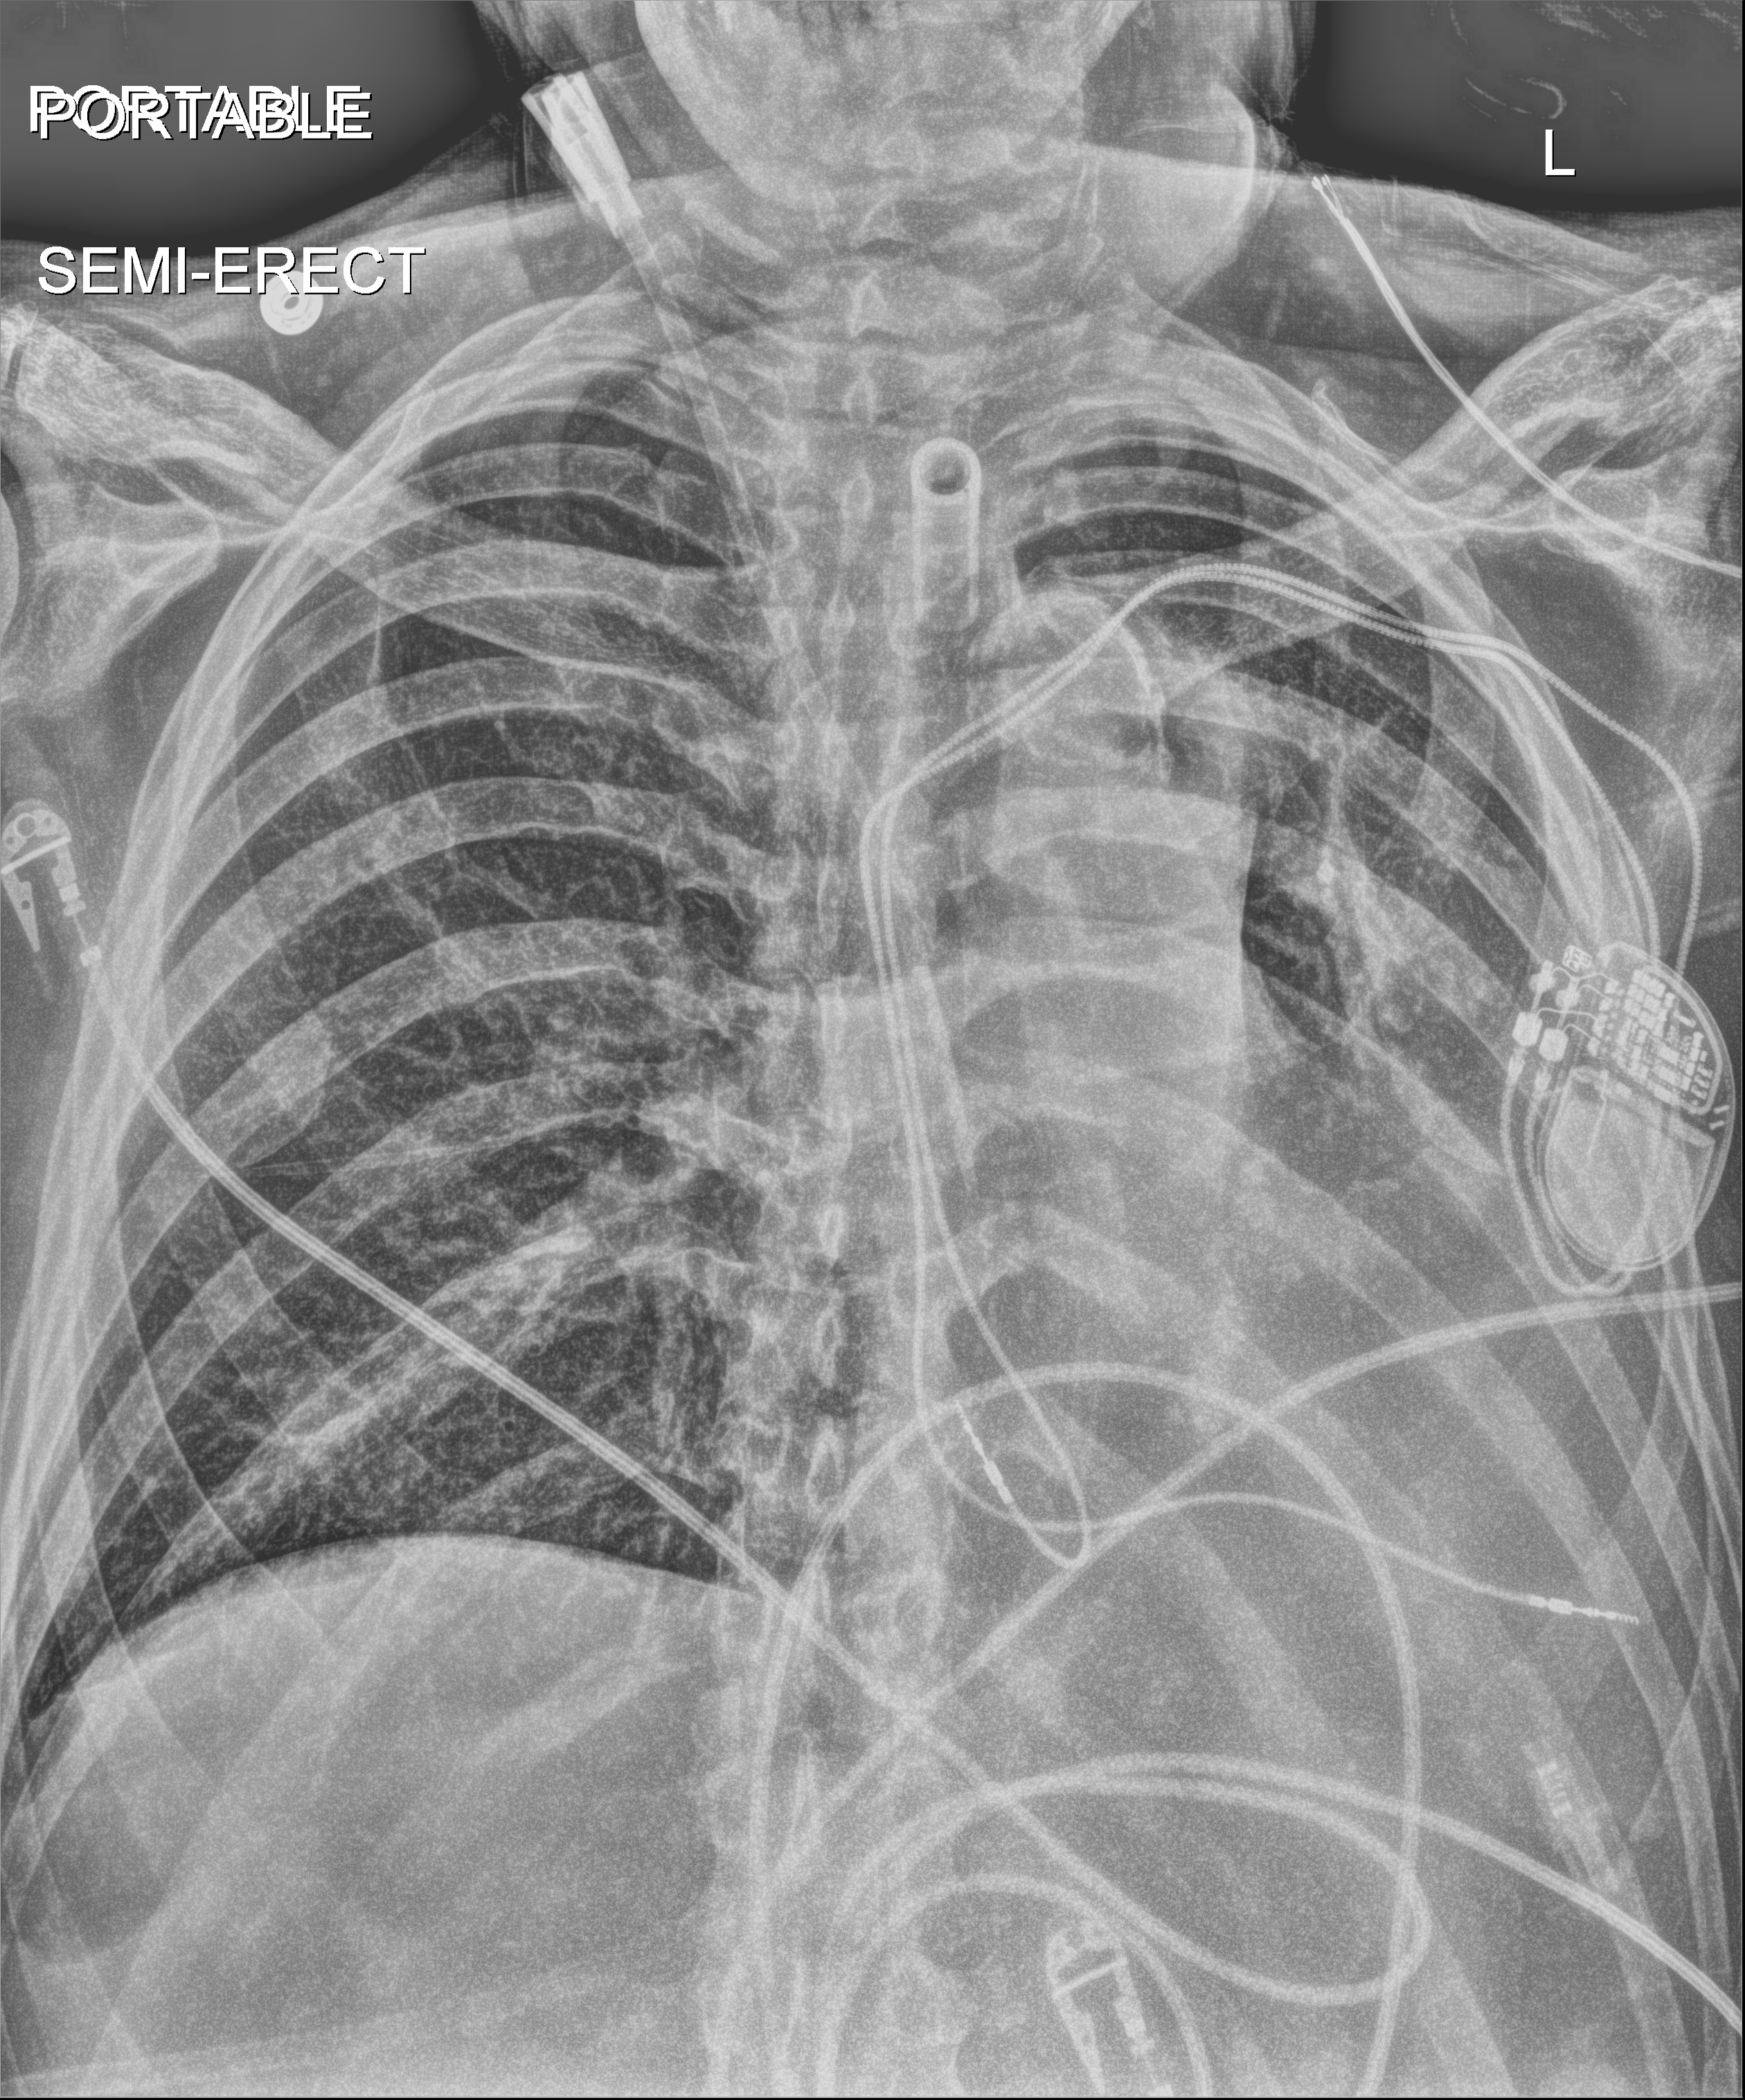
Chest X-ray (portable); anteroposterior (AP) projection. Male patient hospitalised with COVID-19, age 60–74 years.
Hospital-stay facts (about this admission, not read from this image; timing relative to this image not recorded):
- admitted to intensive care during this hospital stay: yes